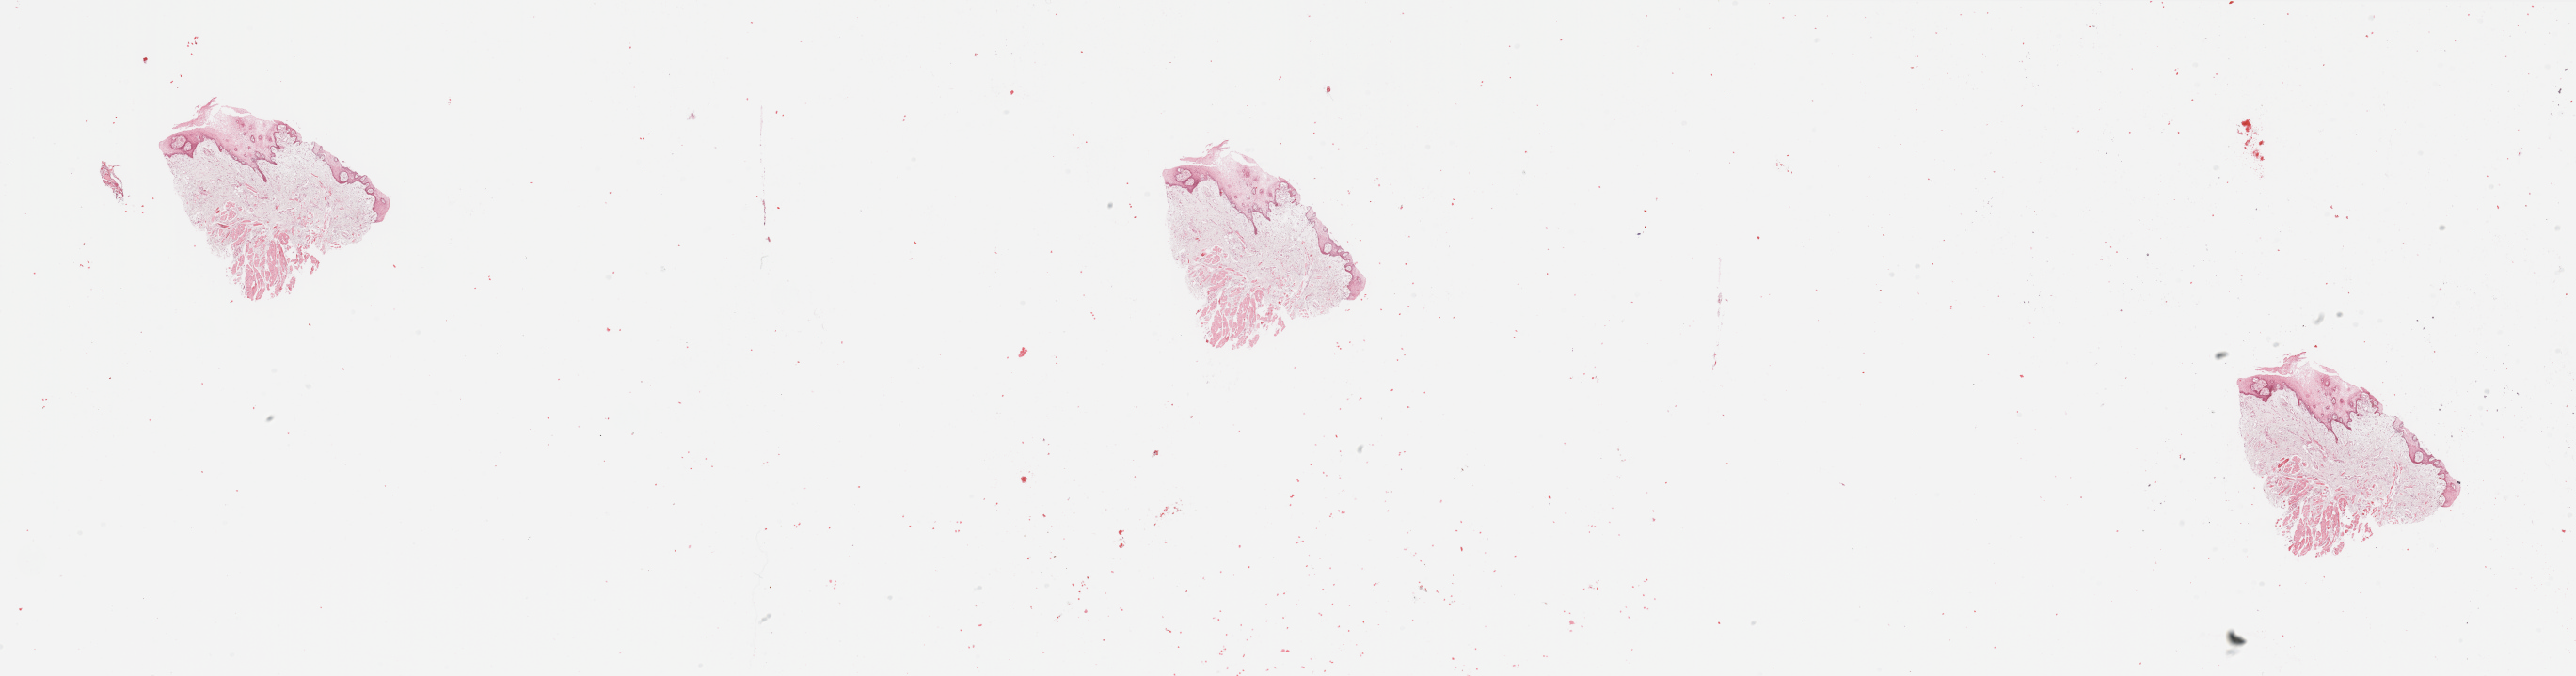
Digitized H&E-stained tissue section (whole slide), shown as a low-resolution overview of the whole scanned area (about 43.3 x 11.4 mm, slide scanned at 20x); normal (non-tumour) tissue sample, sampled site: floor of mouth. Patient: male, age 61 years.
This section: normal (non-tumour) tissue from the same patient. Patient diagnosis: Squamous cell carcinoma, NOS (floor of mouth, NOS).